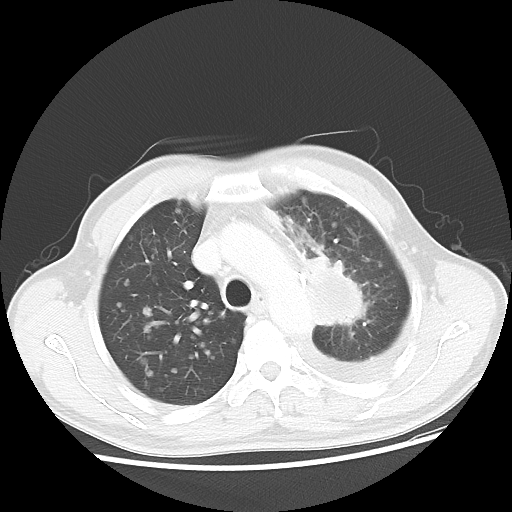
Chest CT, one axial slice; slice 34 of 47 in the series (ordered by position); reconstruction kernel LUNG; 100 kVp; lung window (W 1500 / L -600 HU); 5 mm slice thickness; 512 × 512 image matrix, field of view 362 × 362 mm. Male patient, age 55 years. From the clinical record (not read from this slice): clinical TNM (as recorded): T2 N3 M1a; histopathological grade: G3.
Structures marked on this image (rectangle marked by the reading radiologist):
- lung tumour (recorded histology: squamous cell carcinoma): bounding box <299,248,377,349> (left, top, right, bottom; pixels)